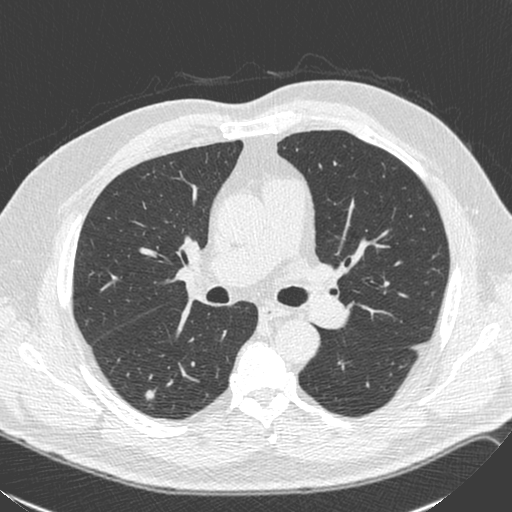
Axial slice from a low-dose chest CT screening exam. Baseline screening round. Lung window (W 1500 / L -600 HU). 1.3 mm slice thickness. 120 kVp. Male participant, aged 71 years at enrolment. Former smoker at enrolment.
- Lesion marked by an expert reader, bounding box (x1, y1, x2, y2) in pixels: (139, 381, 171, 408).
- Reader record for this screening exam (exam-level; its link to the box is not recorded): non-calcified nodule or mass ≥4 mm, right lower lobe, 6 × 6 mm, smooth margins, soft tissue attenuation.
- Lung cancer was diagnosed 231 days after this screen: squamous cell carcinoma, NOS, right lower lobe, poorly differentiated (G3), stage IA (AJCC 6th edition), 4 mm at pathology.